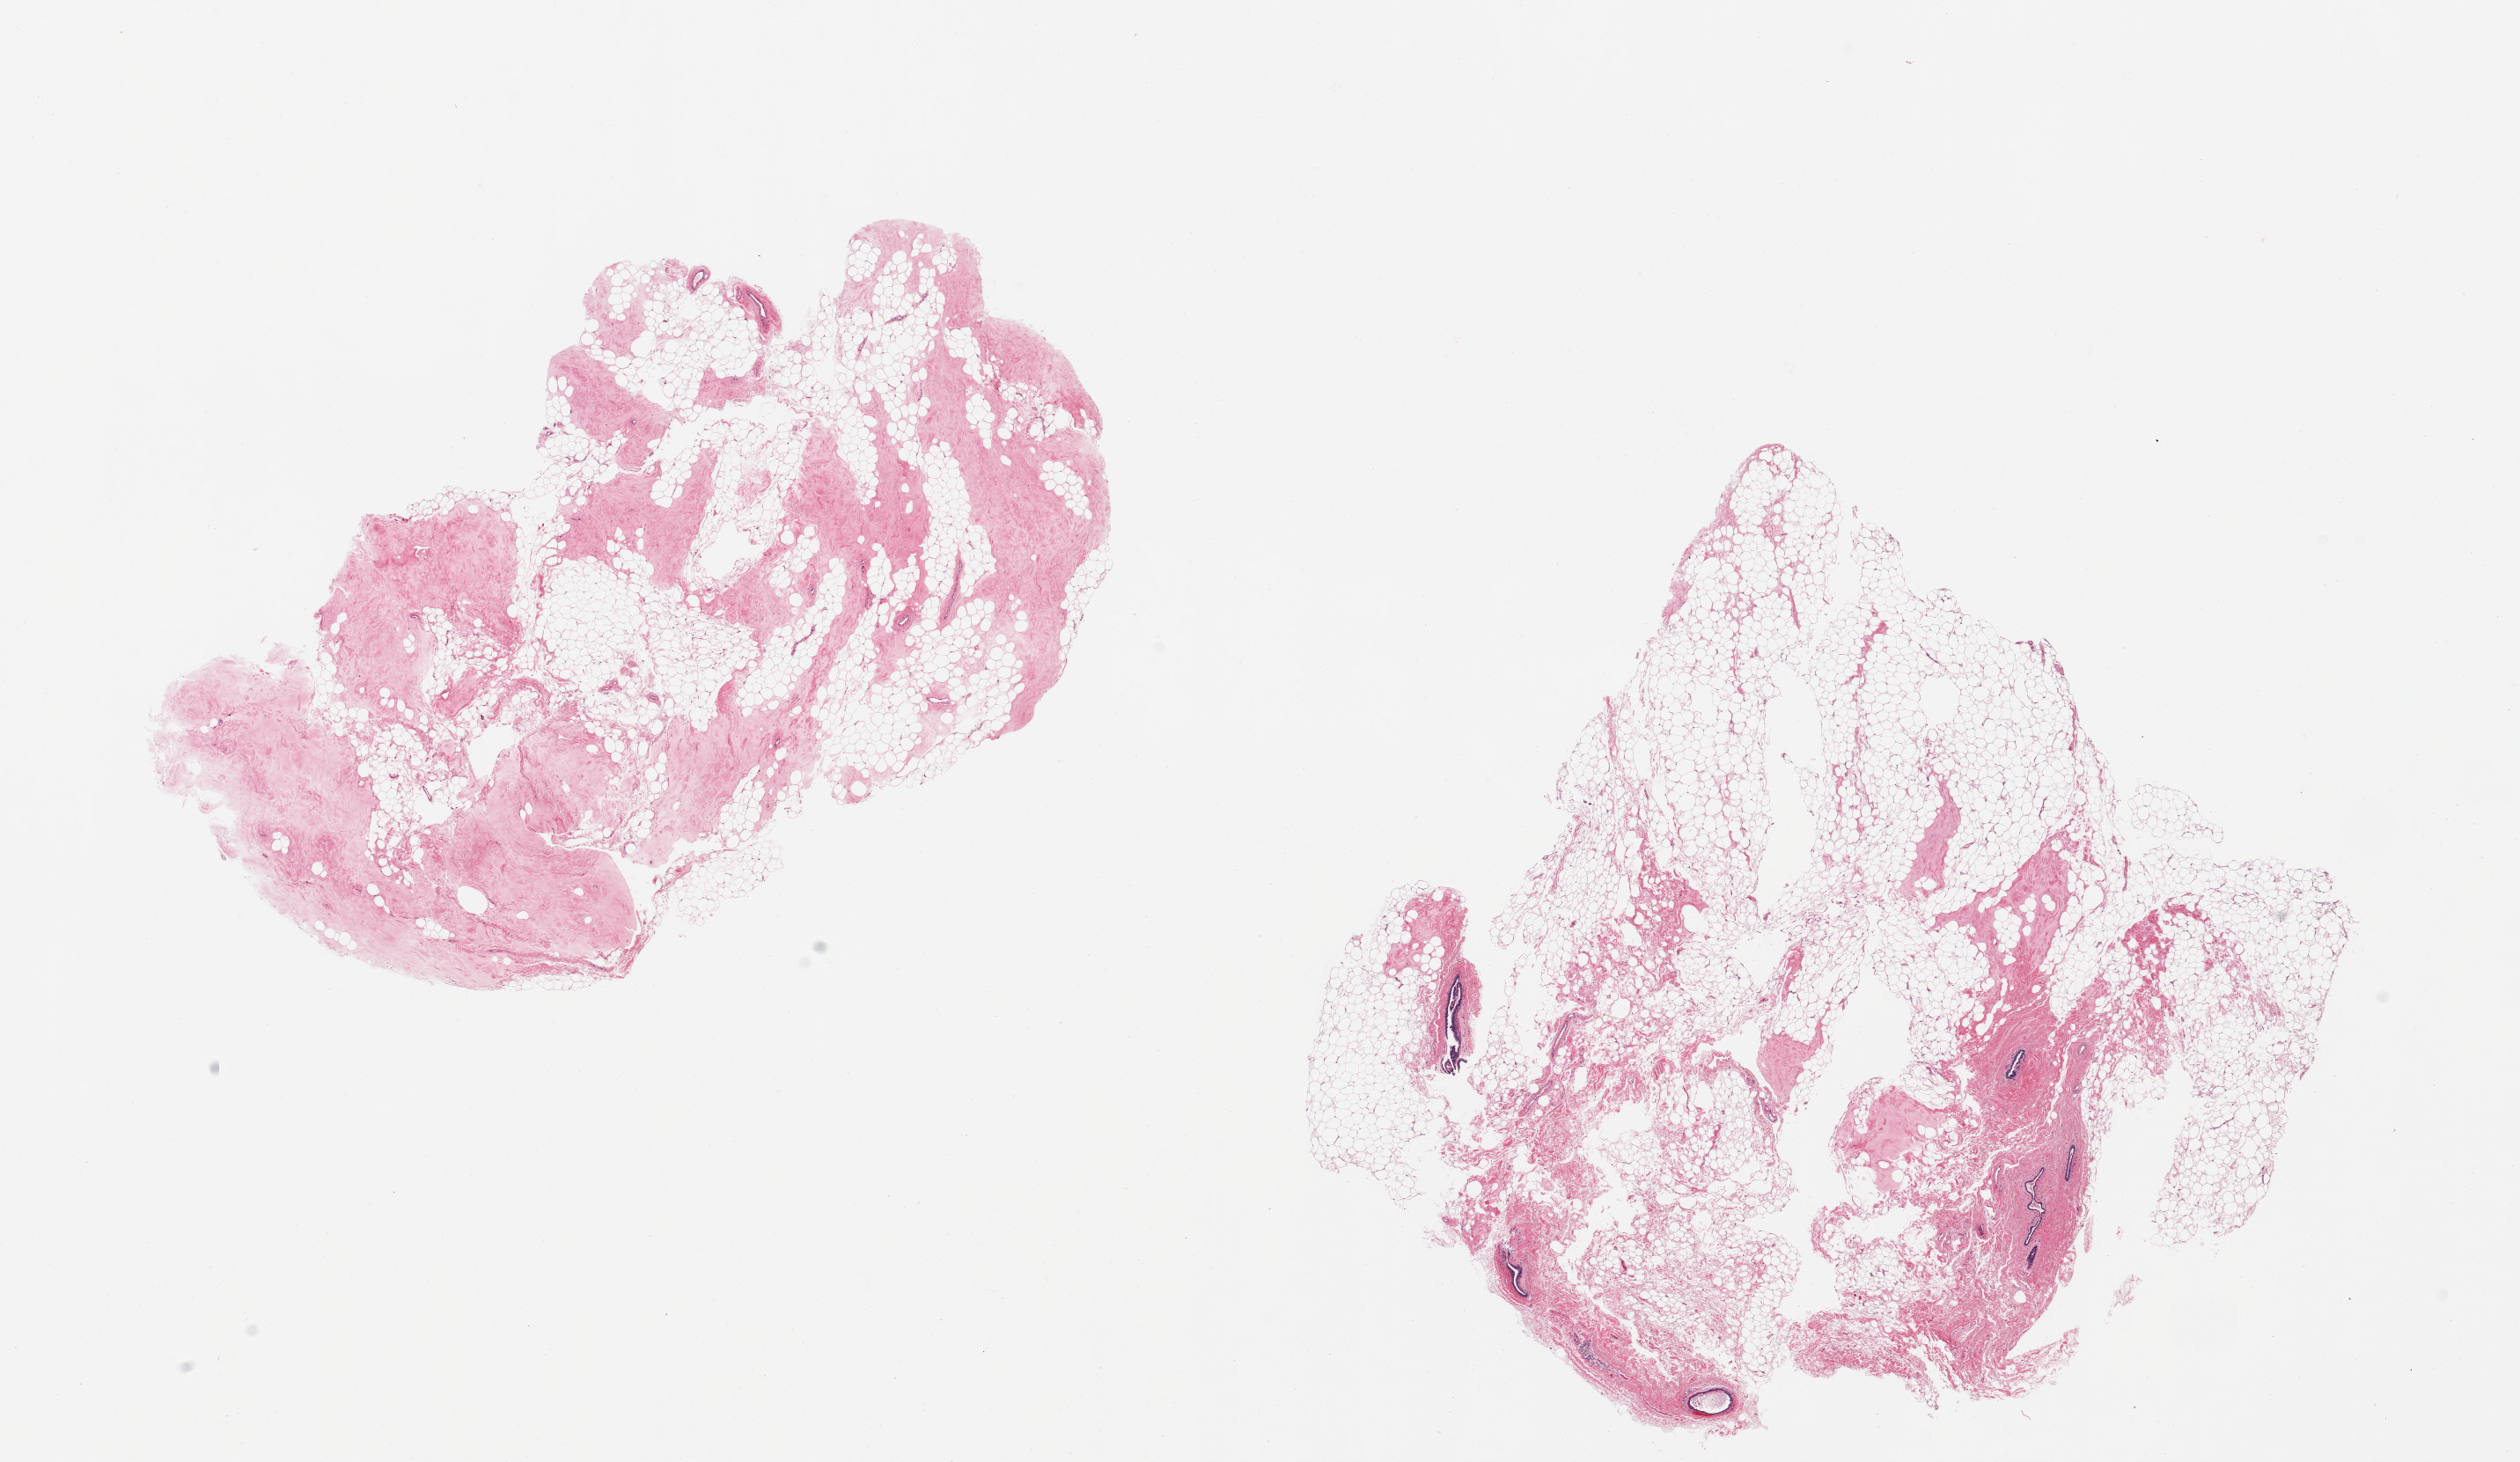
H&E whole-slide image — a low-resolution overview of the entire scanned area, about 22.6 x 13.1 mm; PAXgene-fixed, paraffin-embedded tissue; section of breast (target tissue); donor tissue sample. Donor: female.
* pathologist's review note for this sample: 2 pieces; dense fibrous and adipose stroma (~50:50 and ~25:75), atrophic ductal structures, confined to one piece